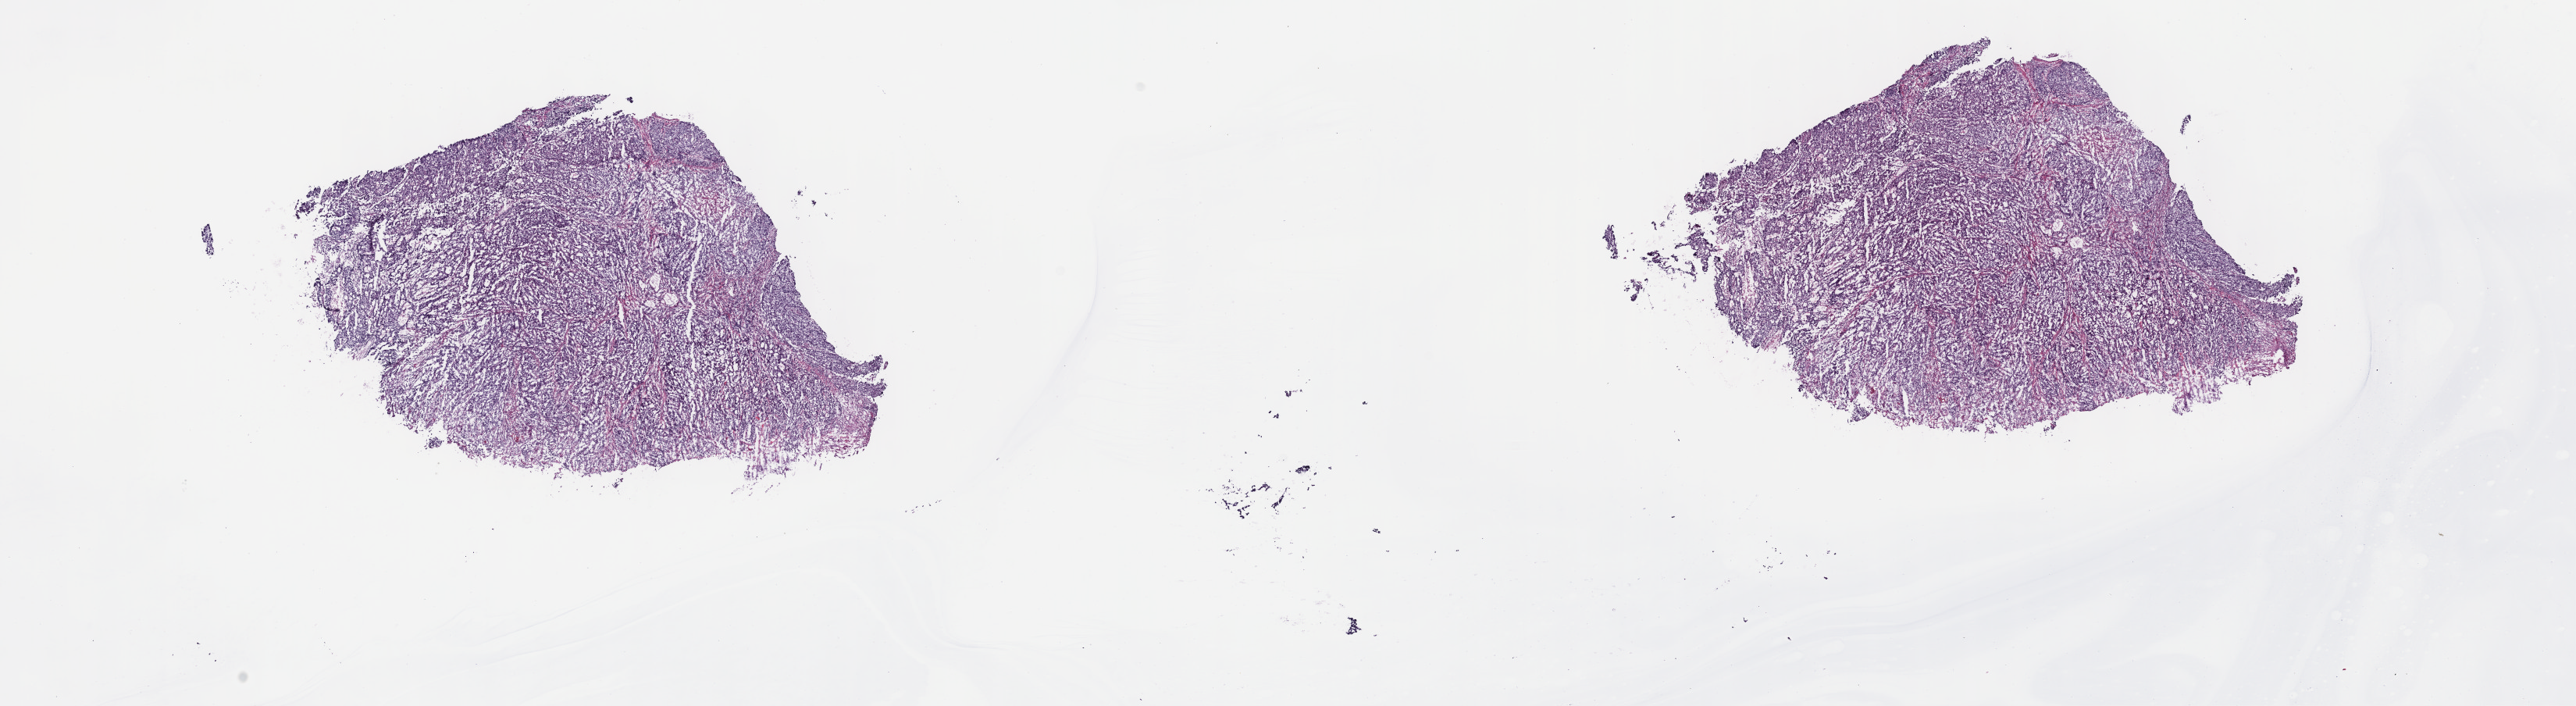
Digitized Hematoxylin and eosin (H&E) stained tissue section (whole slide) — low-resolution overview of the scanned area, about 26.7 x 7.3 mm (from a 40x scan), frozen section, sample: primary tumour, stomach. Female patient; age at initial diagnosis 69 years. Histologic grade: G2 (moderately differentiated). Pathologist review of this section (percent, as recorded): tumour cells 75%, tumour nuclei 80%, normal cells 10%, stromal cells 15%, necrosis 0%. Inflammatory infiltration, as recorded: lymphocyte infiltration 0%, monocyte infiltration 0%, neutrophil infiltration 0%.
AJCC pathologic stage: IIA (7th edition). Diagnosis: Tubular adenocarcinoma (cardia, NOS).